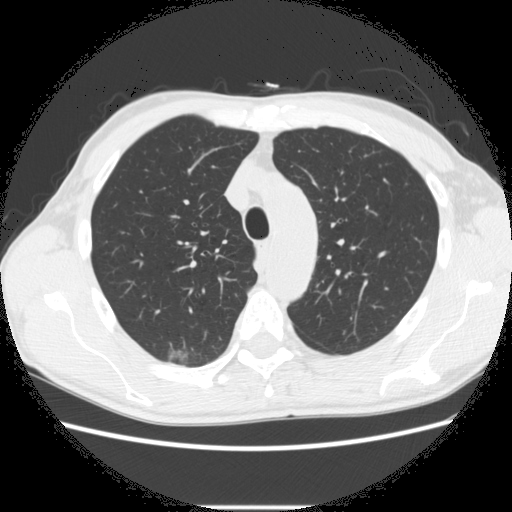
Axial slice from a low-dose chest CT screening exam, second screening round (one year after baseline), lung window (W 1500 / L -600 HU), standard (soft-tissue) reconstruction kernel (STANDARD), 120 kVp, slice 72 of 282 in the series. Male participant, aged 66 years at enrolment. Former smoker at enrolment.
- Expert-annotated lung lesion, bounding box (x1, y1, x2, y2) in pixels: (159, 335, 223, 370).
- The screening reader recorded 5 non-calcified nodules or masses ≥4 mm on this exam (right lower lobe, right upper lobe, right upper lobe, right upper lobe, left lower lobe); which of them this box marks is not recorded.
- Official screen result: positive, change unspecified: nodule(s) >= 4 mm or enlarging nodule(s), mass(es), or other non-specific abnormalities suspicious for lung cancer.
- Participant outcome: lung cancer diagnosed 75 days after this screen — adenocarcinoma, NOS, right upper lobe, undifferentiated (G4), stage IA (AJCC 6th edition), 20 mm at pathology.